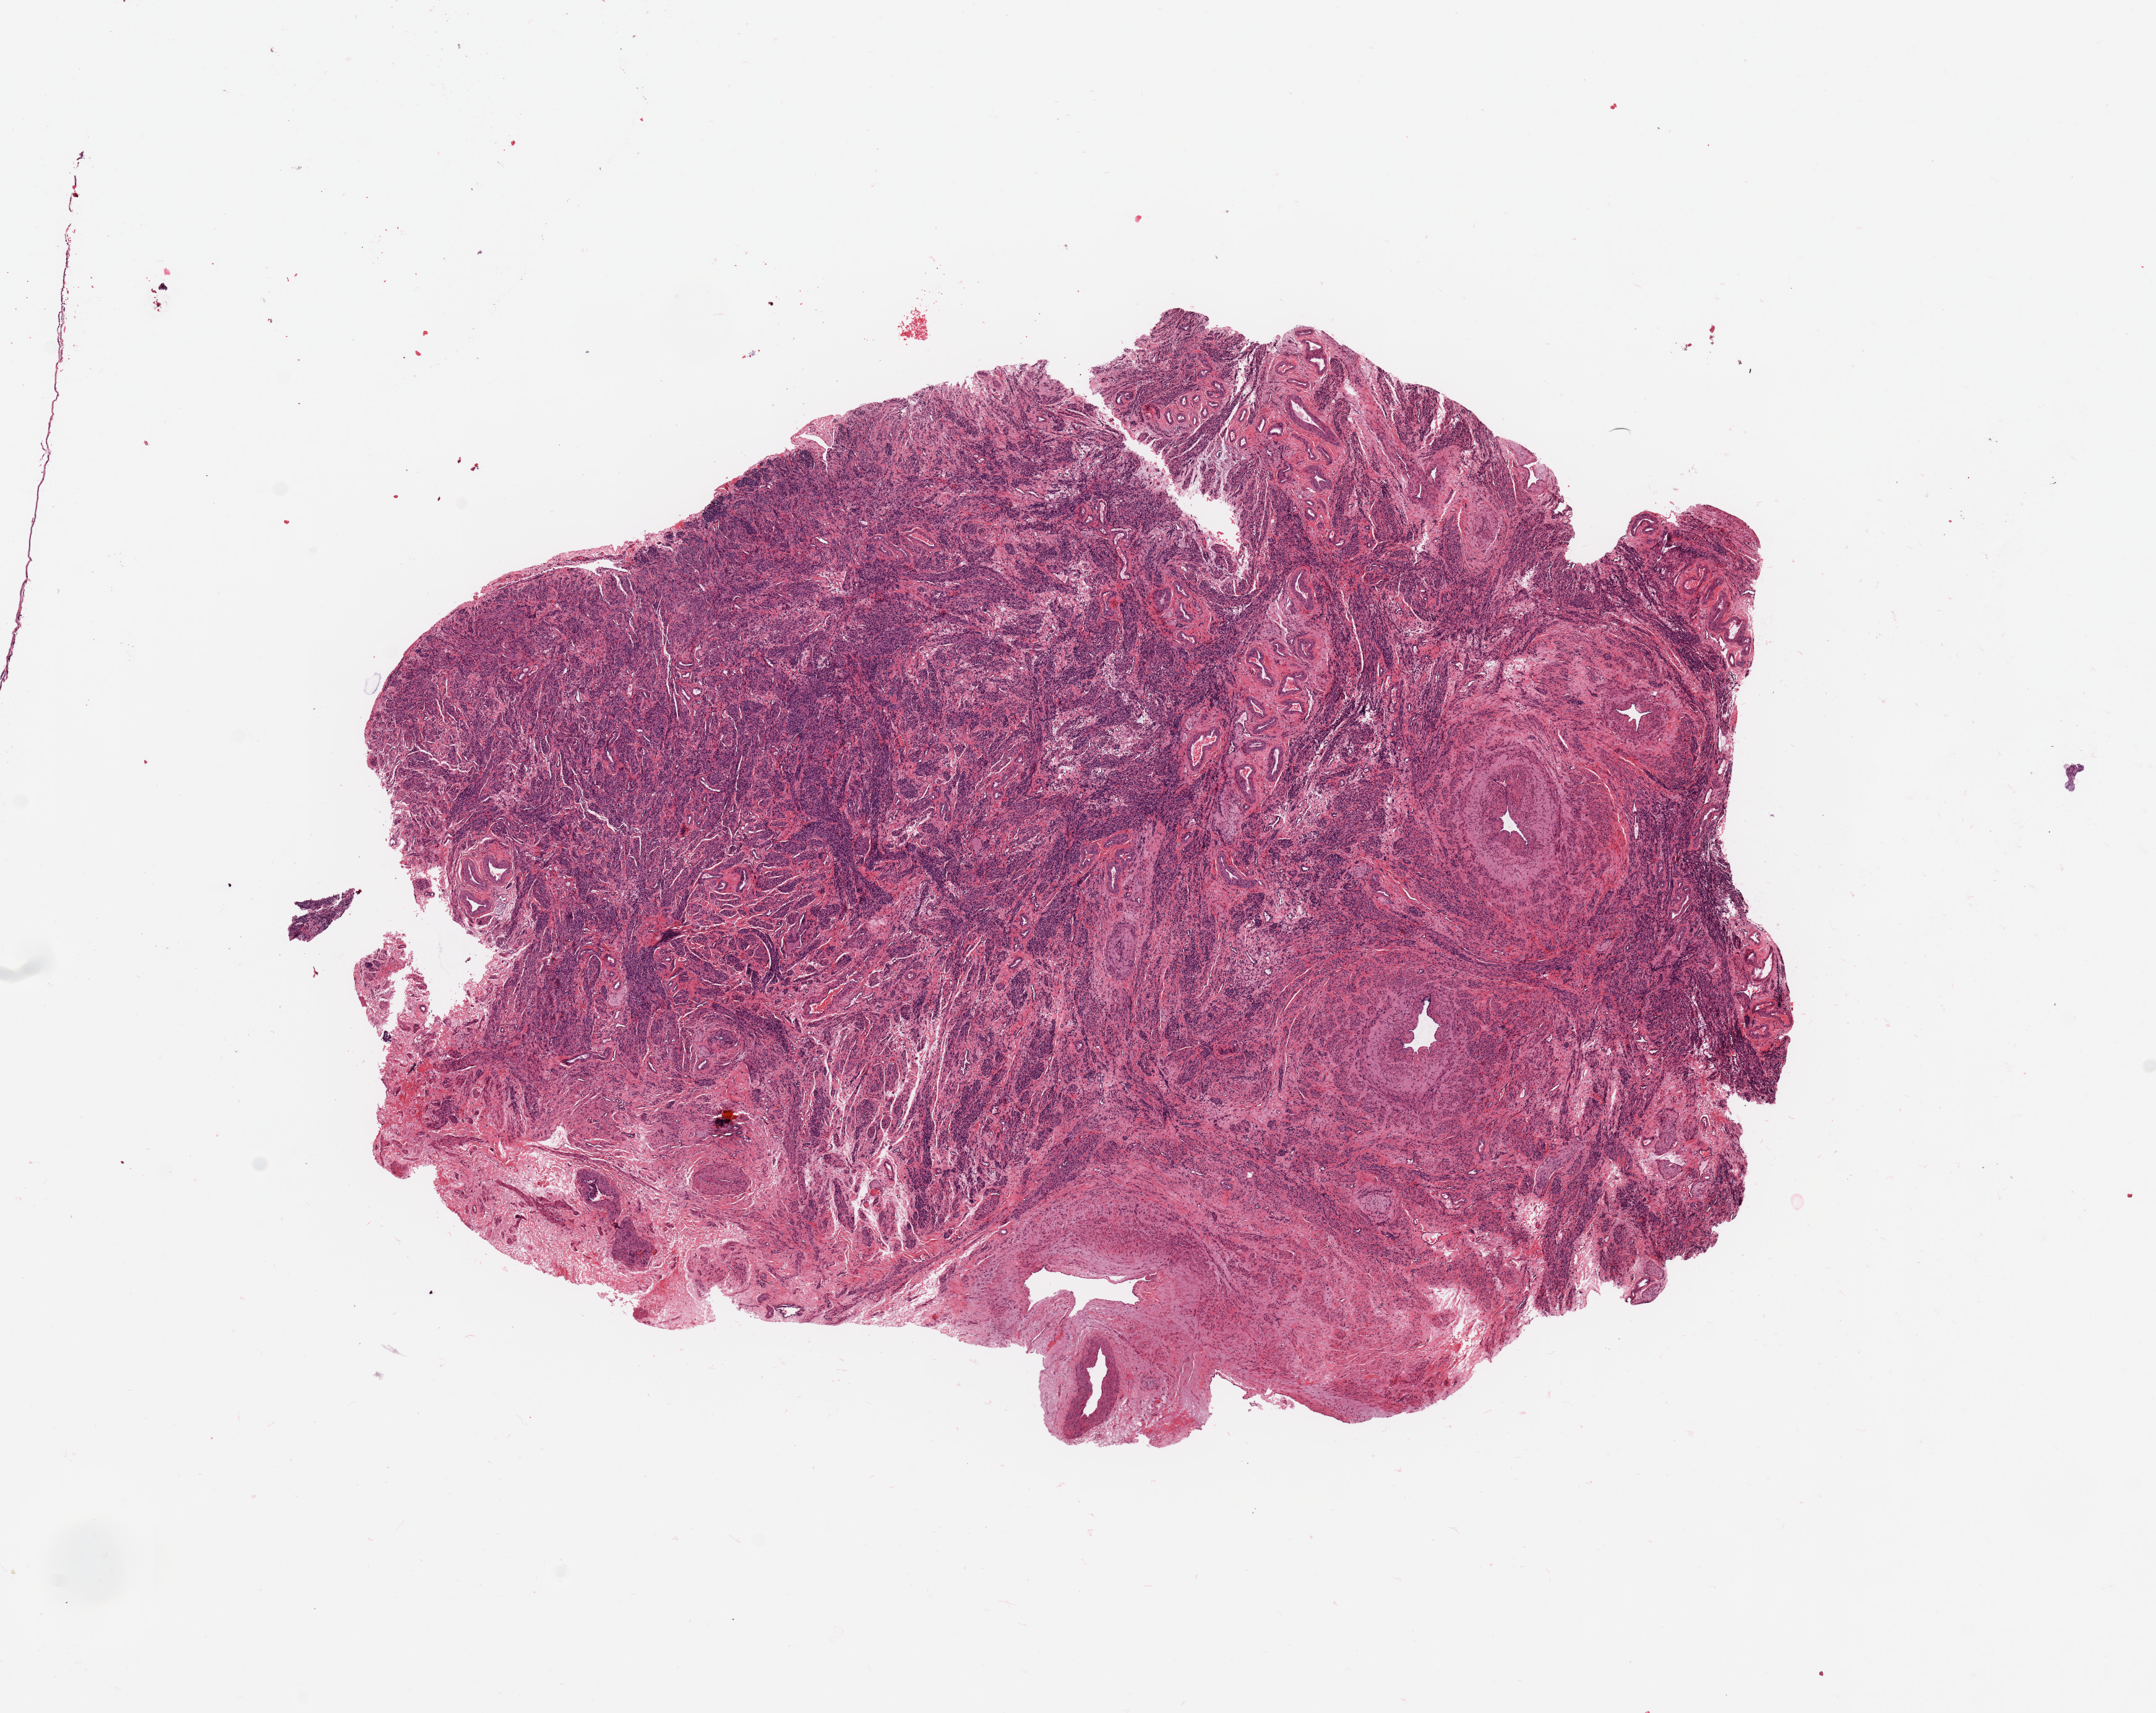
Whole-slide histology image, Hematoxylin and eosin (H&E) stained — low-resolution overview of the scanned area, about 13.8 x 11.0 mm (from a 20x scan); normal (non-tumour) tissue sample, uterus. 65-year-old female patient.
* this section: normal (non-tumour) tissue from the same patient
* patient diagnosis: Endometrioid adenocarcinoma, NOS